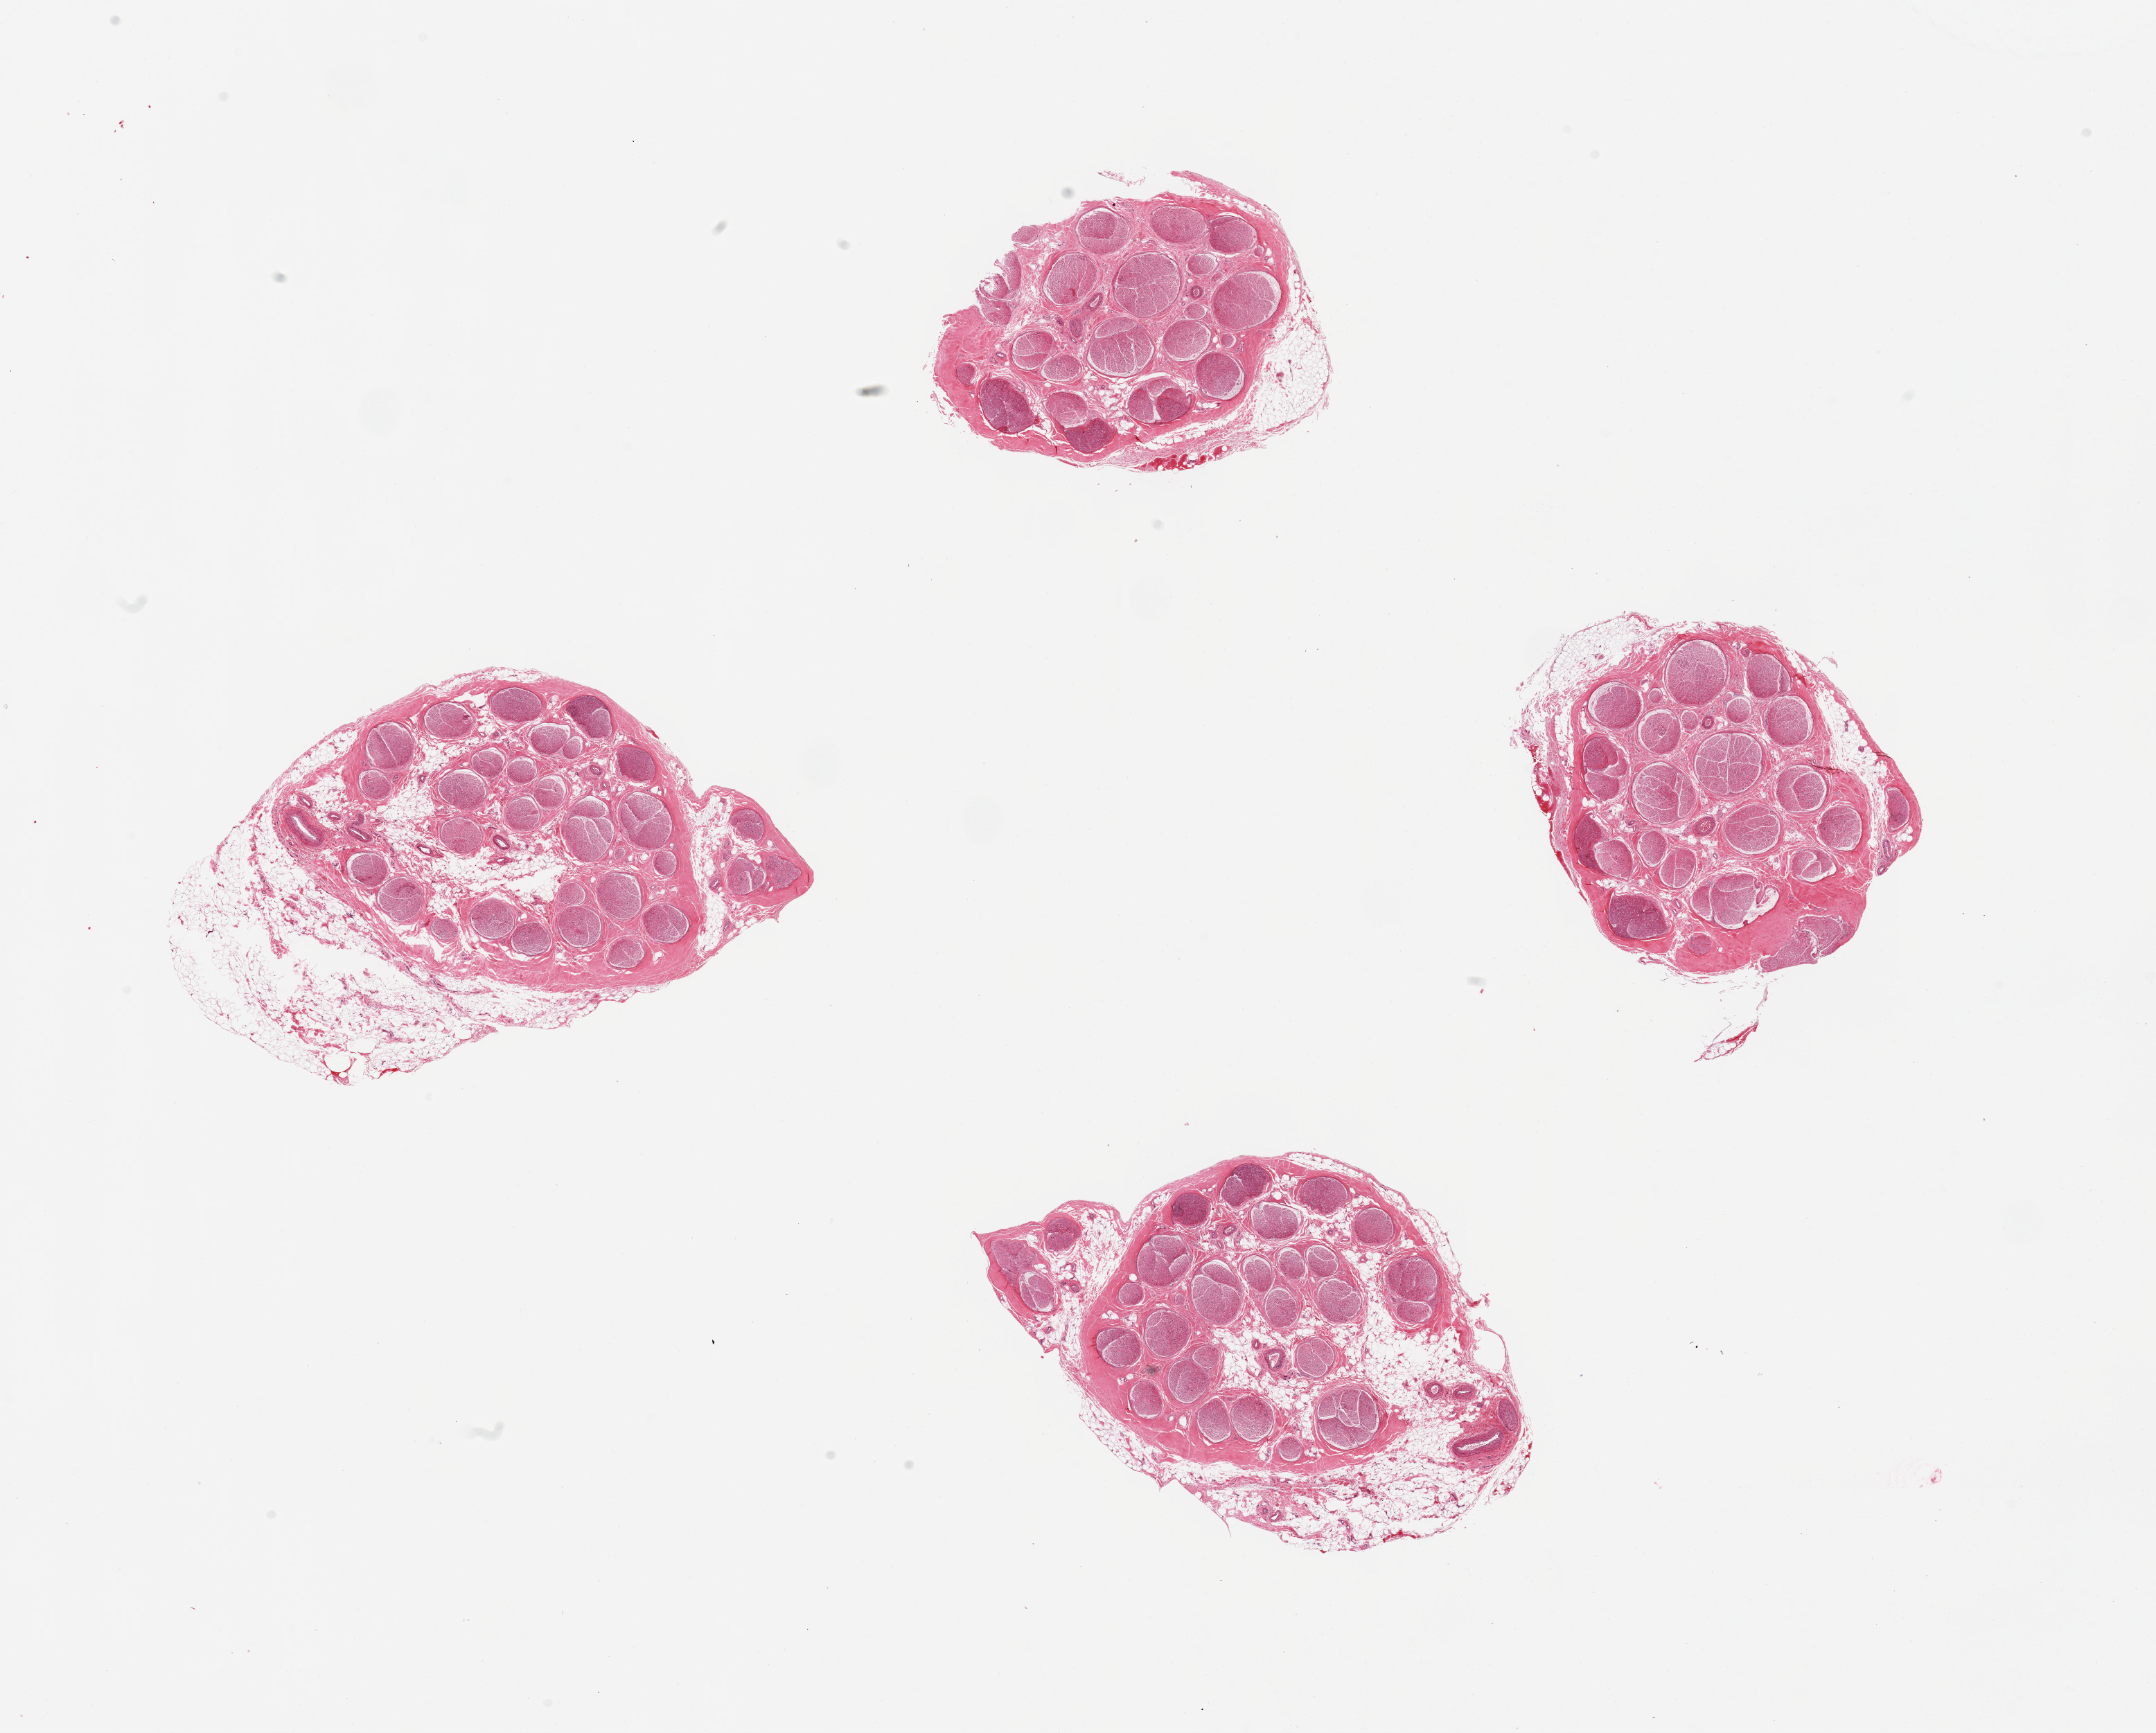
Digitized H&E-stained section, shown as a low-resolution overview of the whole scanned area (about 24.6 x 19.8 mm); PAXgene-fixed, paraffin-embedded tissue; sampled site (target tissue): tibial nerve; tissue donor sample. Donor sex: male.
Pathologist's review note for this sample: 4 pieces; 10-40% internal and attached (2mm) fat/vessels.